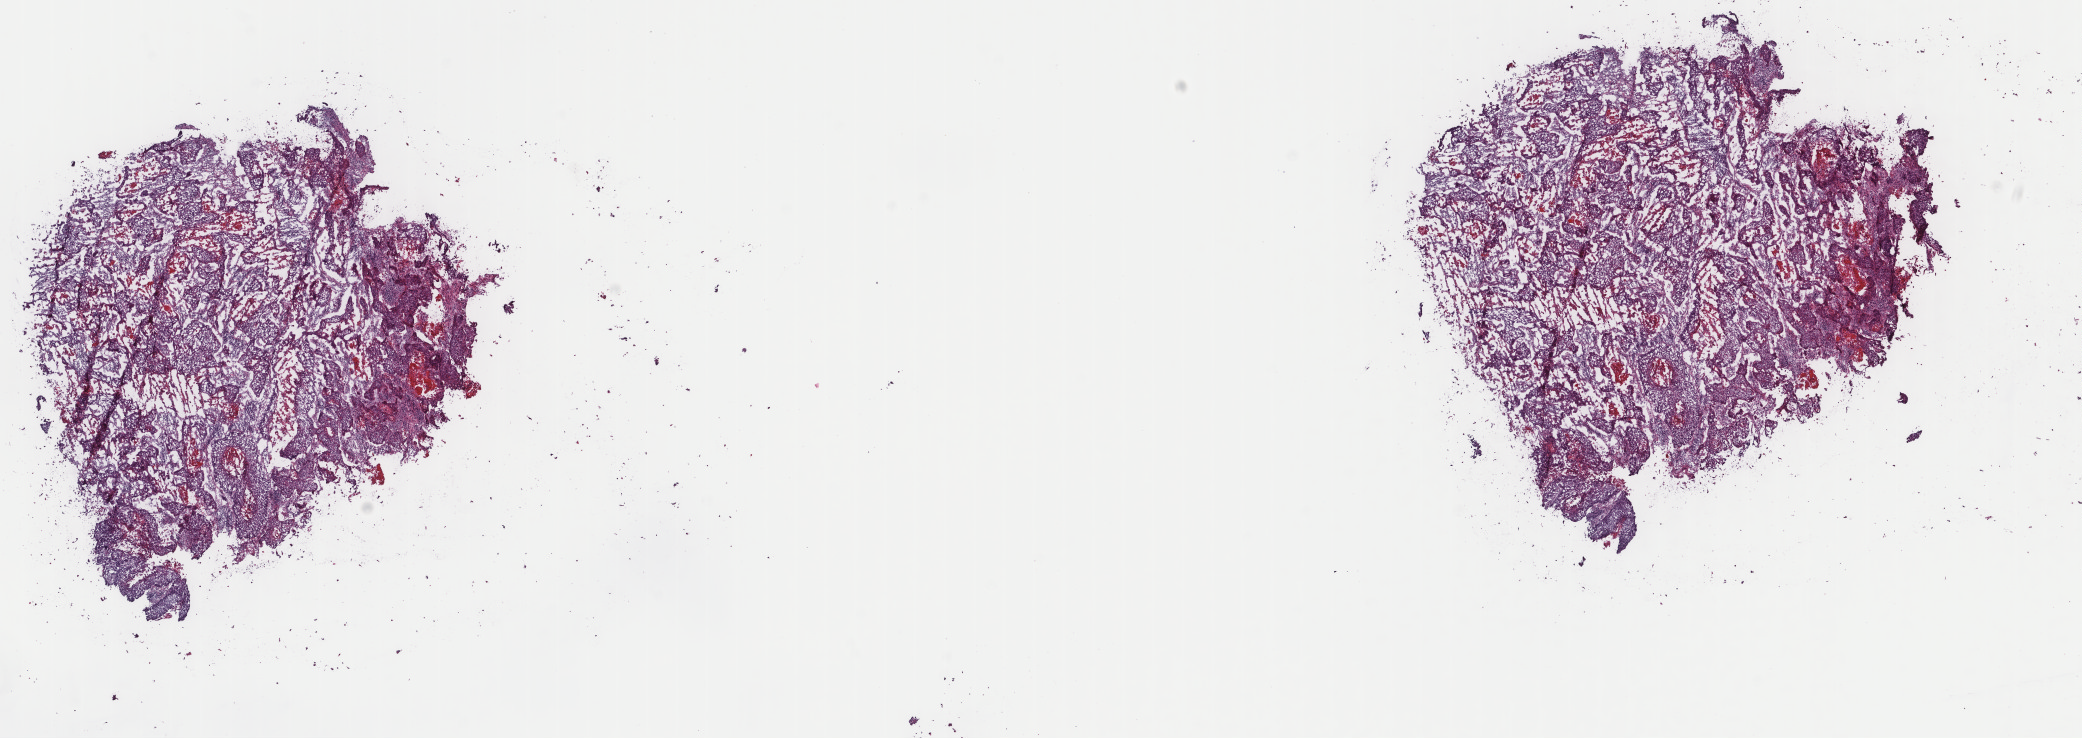
Whole-slide histology image, H&E, low-resolution overview of the scanned area, about 16.5 x 5.9 mm (from a 40x scan), frozen section from the top of the tissue portion, sample: primary tumour, cervix. Female patient; age at initial diagnosis 46 years. Histologic grade: G3 (poorly differentiated). Slide review estimates, as recorded: tumour cells 75%, tumour nuclei 75%, normal cells 0%, stromal cells 20%, necrosis 5%. Inflammatory infiltration, as recorded: lymphocyte infiltration 0%, monocyte infiltration 0%, neutrophil infiltration 0%.
• pathologic diagnosis: Squamous cell carcinoma, NOS (cervix uteri)
• FIGO stage: IIIB